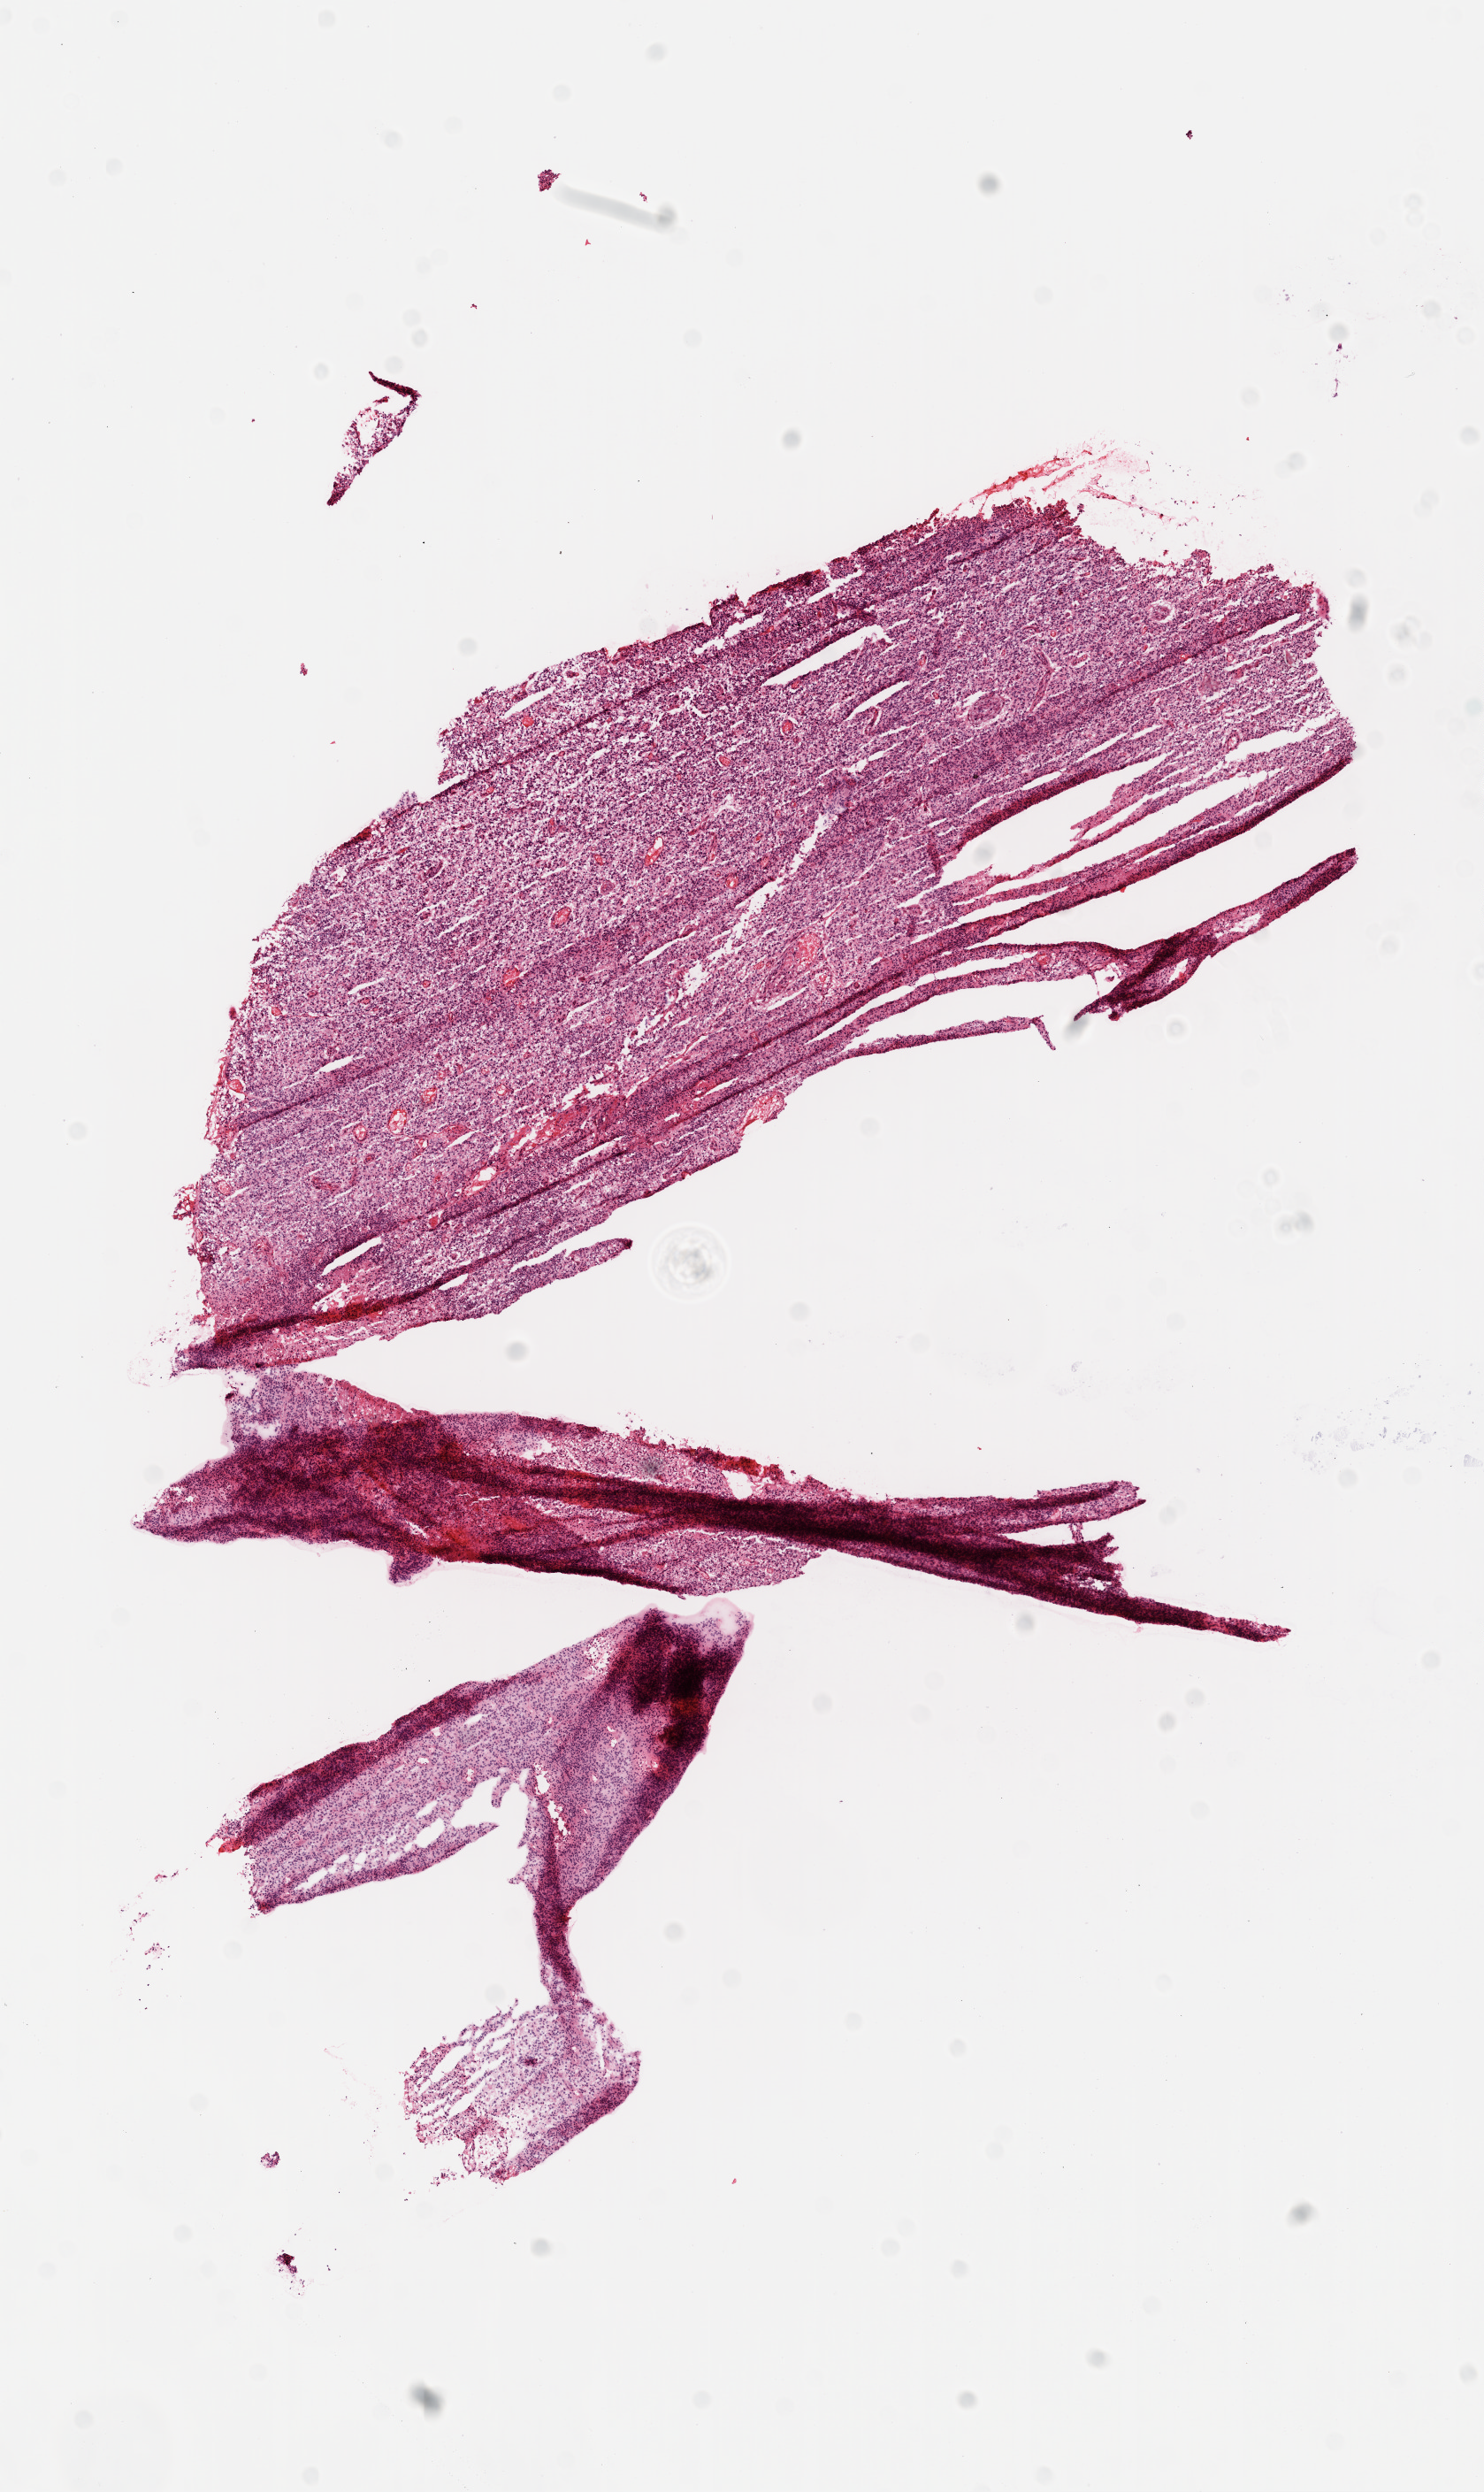
Whole-slide histology image, Hematoxylin and eosin (H&E) stained — a low-resolution overview of the entire scanned area, about 6.8 x 11.4 mm (acquisition: 20x scan); frozen section from the top of the tissue portion; primary tumour sample from the brain. Male, age 50 years at initial diagnosis. Pathologist review of this section (percent, as recorded): tumour cells 100%, tumour nuclei 95%, normal cells 0%, stromal cells 0%, necrosis 0%.
Histologic diagnosis: Glioblastoma.